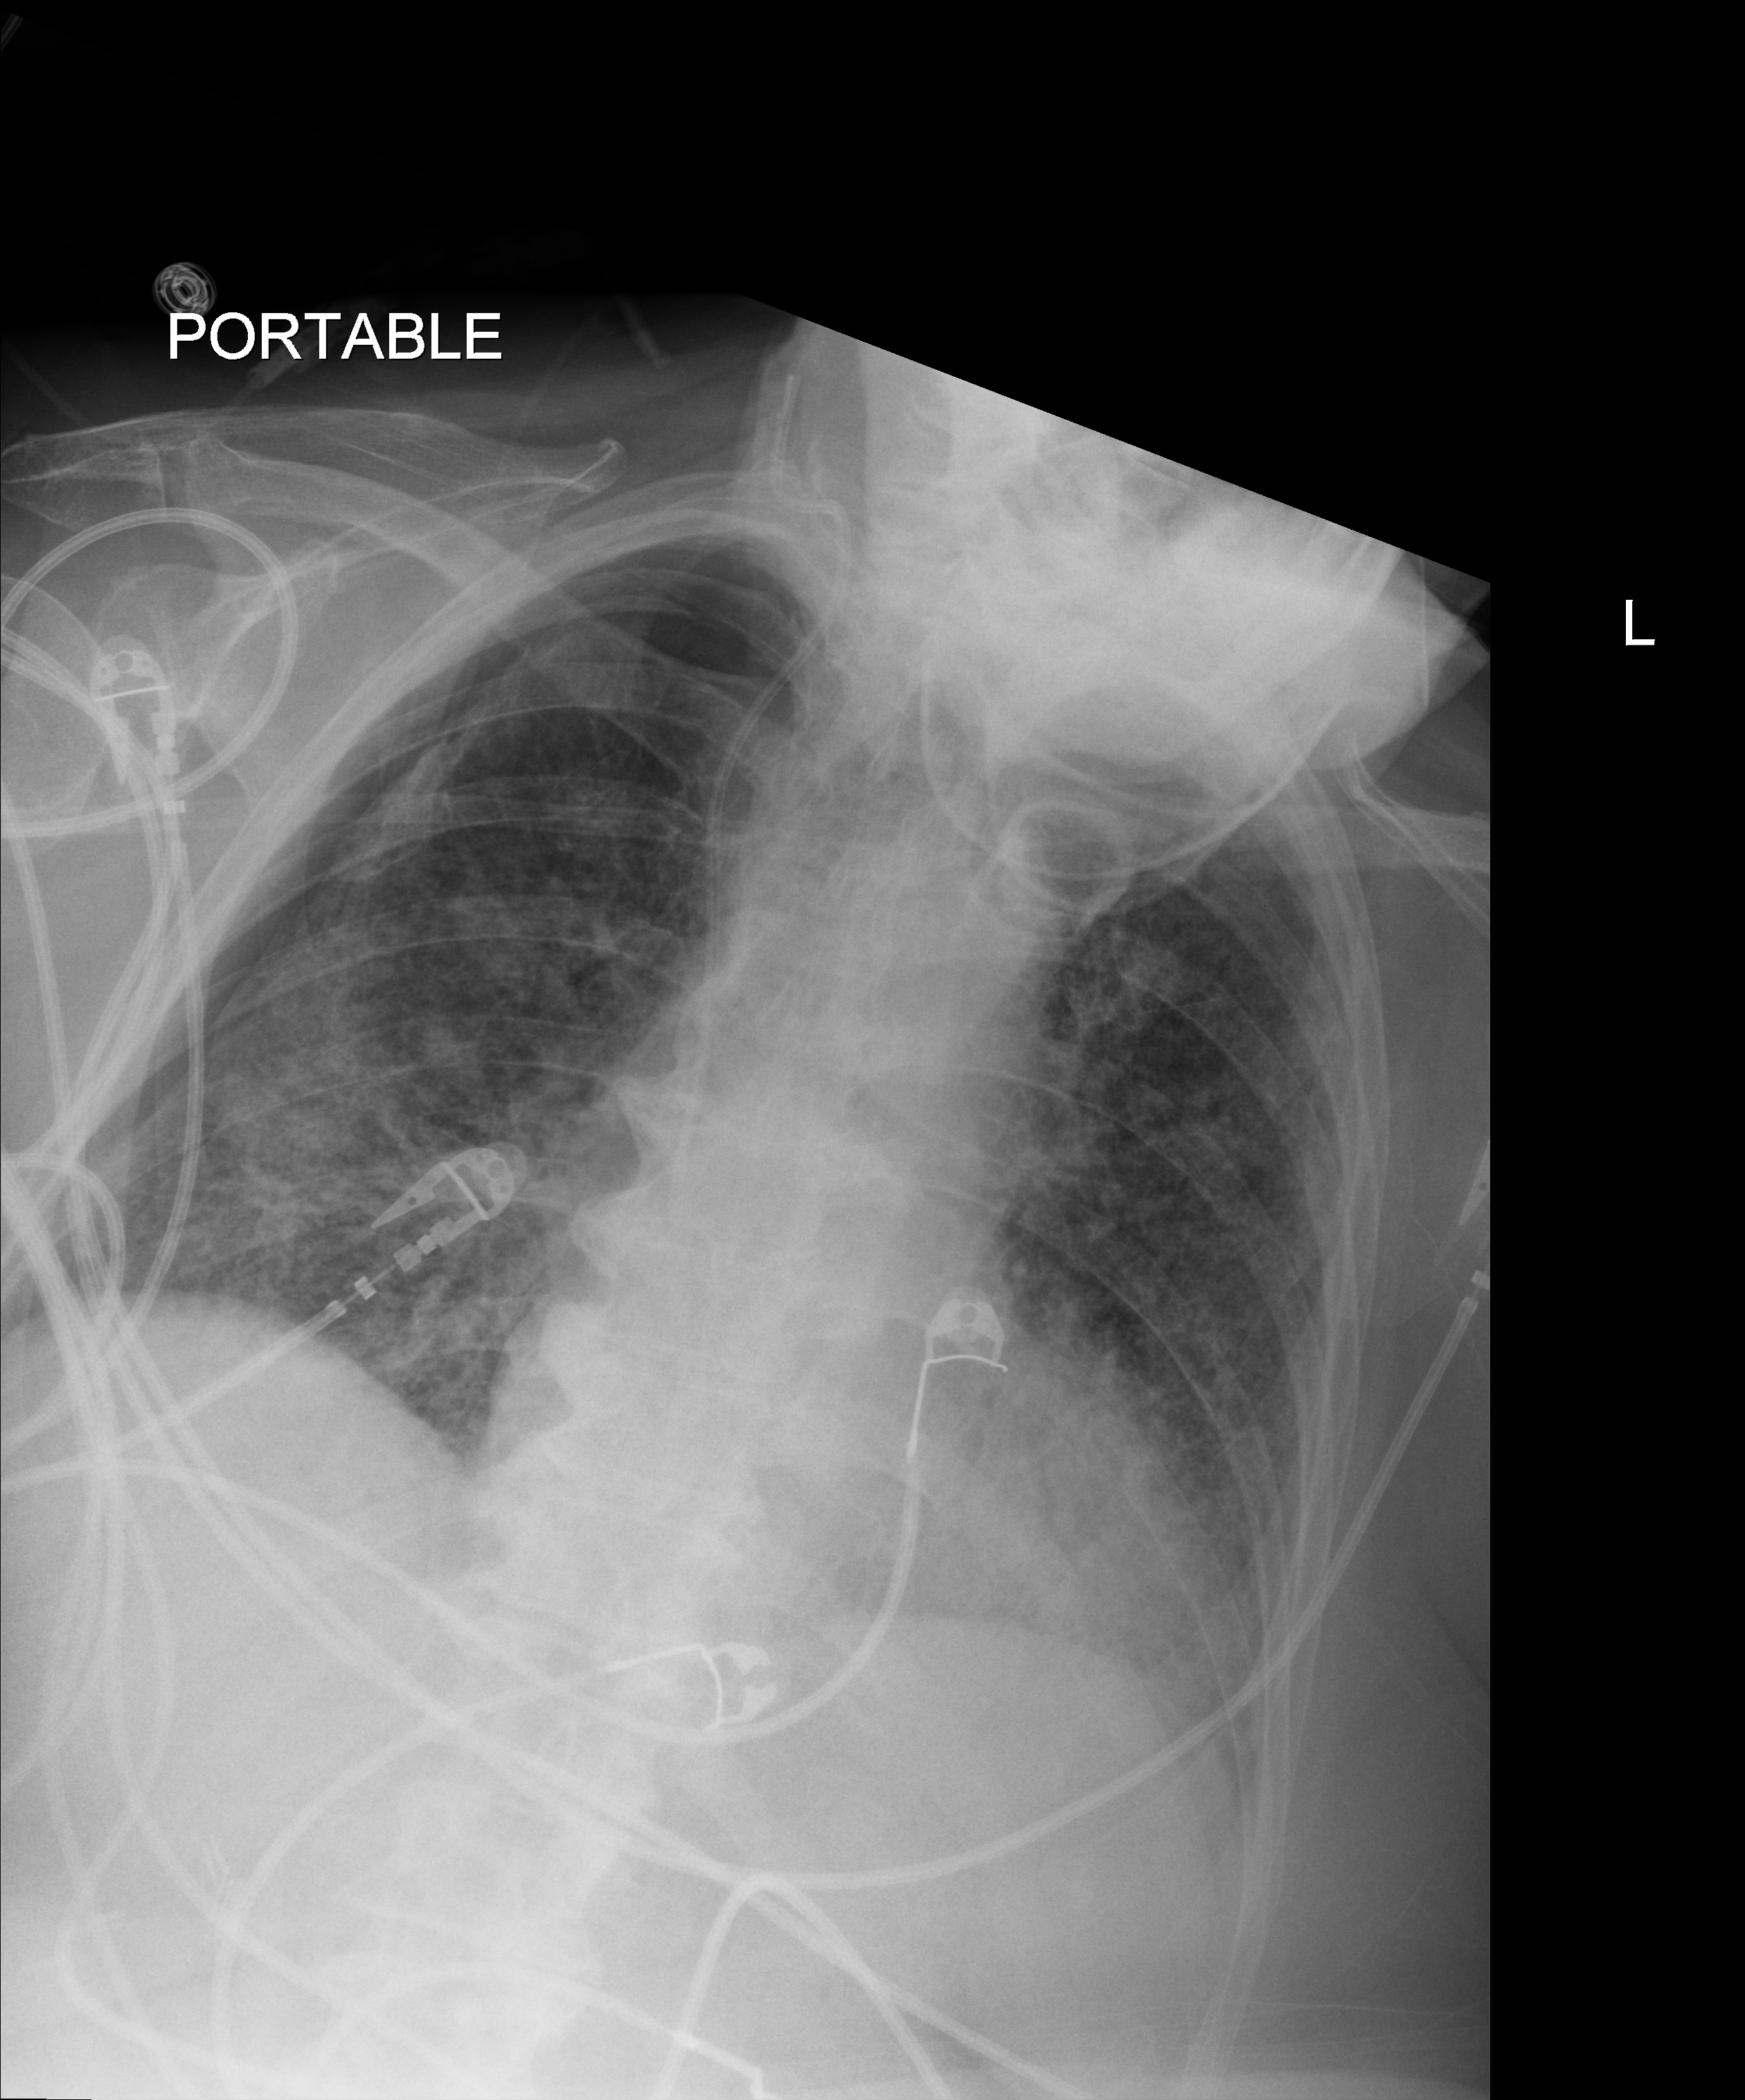
Chest radiograph (digital radiography), anteroposterior (AP) projection. Female patient hospitalised with COVID-19, age 75–90 years.
Admission-level facts for this patient (not findings on this image; timing relative to this image not recorded):
- admitted to intensive care during this hospital stay: no
- smoking status (admission record): former
- mechanically ventilated during this hospital stay: yes